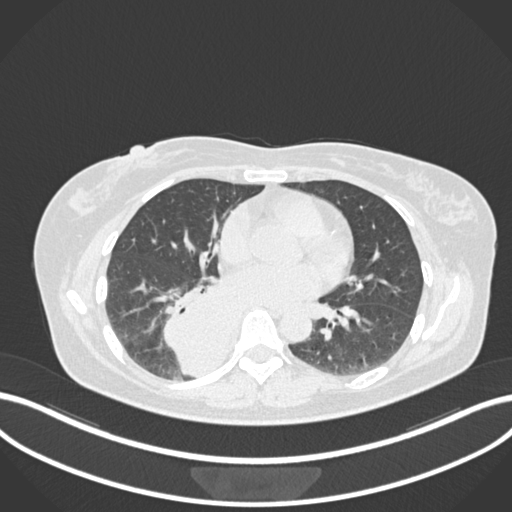
Chest CT, one axial slice; reconstruction kernel B30f; 120 kVp; lung window (W 1500 / L -600 HU); 512 × 512 image matrix, field of view 400 × 400 mm. Female patient, age 54 years. From the clinical record (not read from this slice): clinical TNM (as recorded): T4 N0 M0.
Structures marked on this image (bounding box drawn by a radiologist):
- lung tumour (recorded histology: adenocarcinoma): bounding box <160,276,243,381> (left, top, right, bottom; pixels)